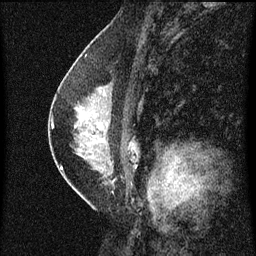
Breast MRI (dynamic contrast-enhanced), one sagittal slice; position 35 of 60 along the scan axis; dynamic contrast-enhanced series, image 2 of 3 at this slice position (ordered by acquisition); 1.5 T; TE 4.2 ms, TR 8 ms; 256 × 256 image matrix, field of view 180 × 180 mm. Female patient, age 47 years.
Structures marked on this image (semi-automatically segmented with operator editing):
- analysis volume of interest (the breast-tissue region the enhancement analysis was run in; not a lesion): bounding box <54,80,135,187> (left, top, right, bottom; pixels)
- tumour enhancement mask (voxels above the 70 % enhancement threshold inside the analysis volume of interest): <54,126,63,169>